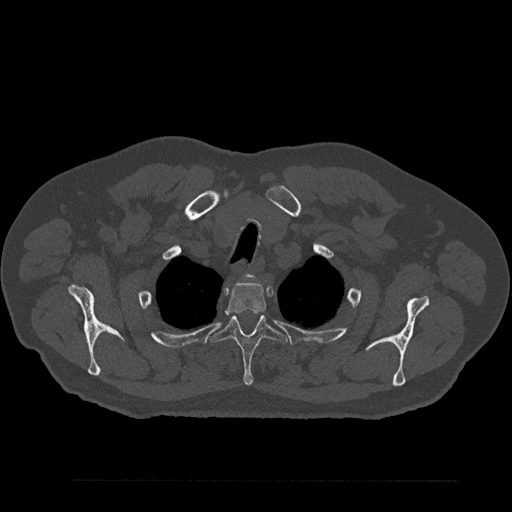
CT including the spine, one axial slice. Position 697 of 797 along the scan axis. Reconstruction kernel Br40s/3. Bone window (W 1800 / L 400 HU). 0.5 mm slice thickness. 512 × 512 image matrix, field of view 430 × 430 mm. Patient: male, 61 years. Case-level facts recorded for this patient, not image findings: primary cancer: prostate.
Annotated regions visible in this slice (semi-automatically segmented with operator editing):
- T2 vertebra: bounding box <226,281,267,314> (left, top, right, bottom; pixels)
- T3 vertebra: <212,315,286,386>